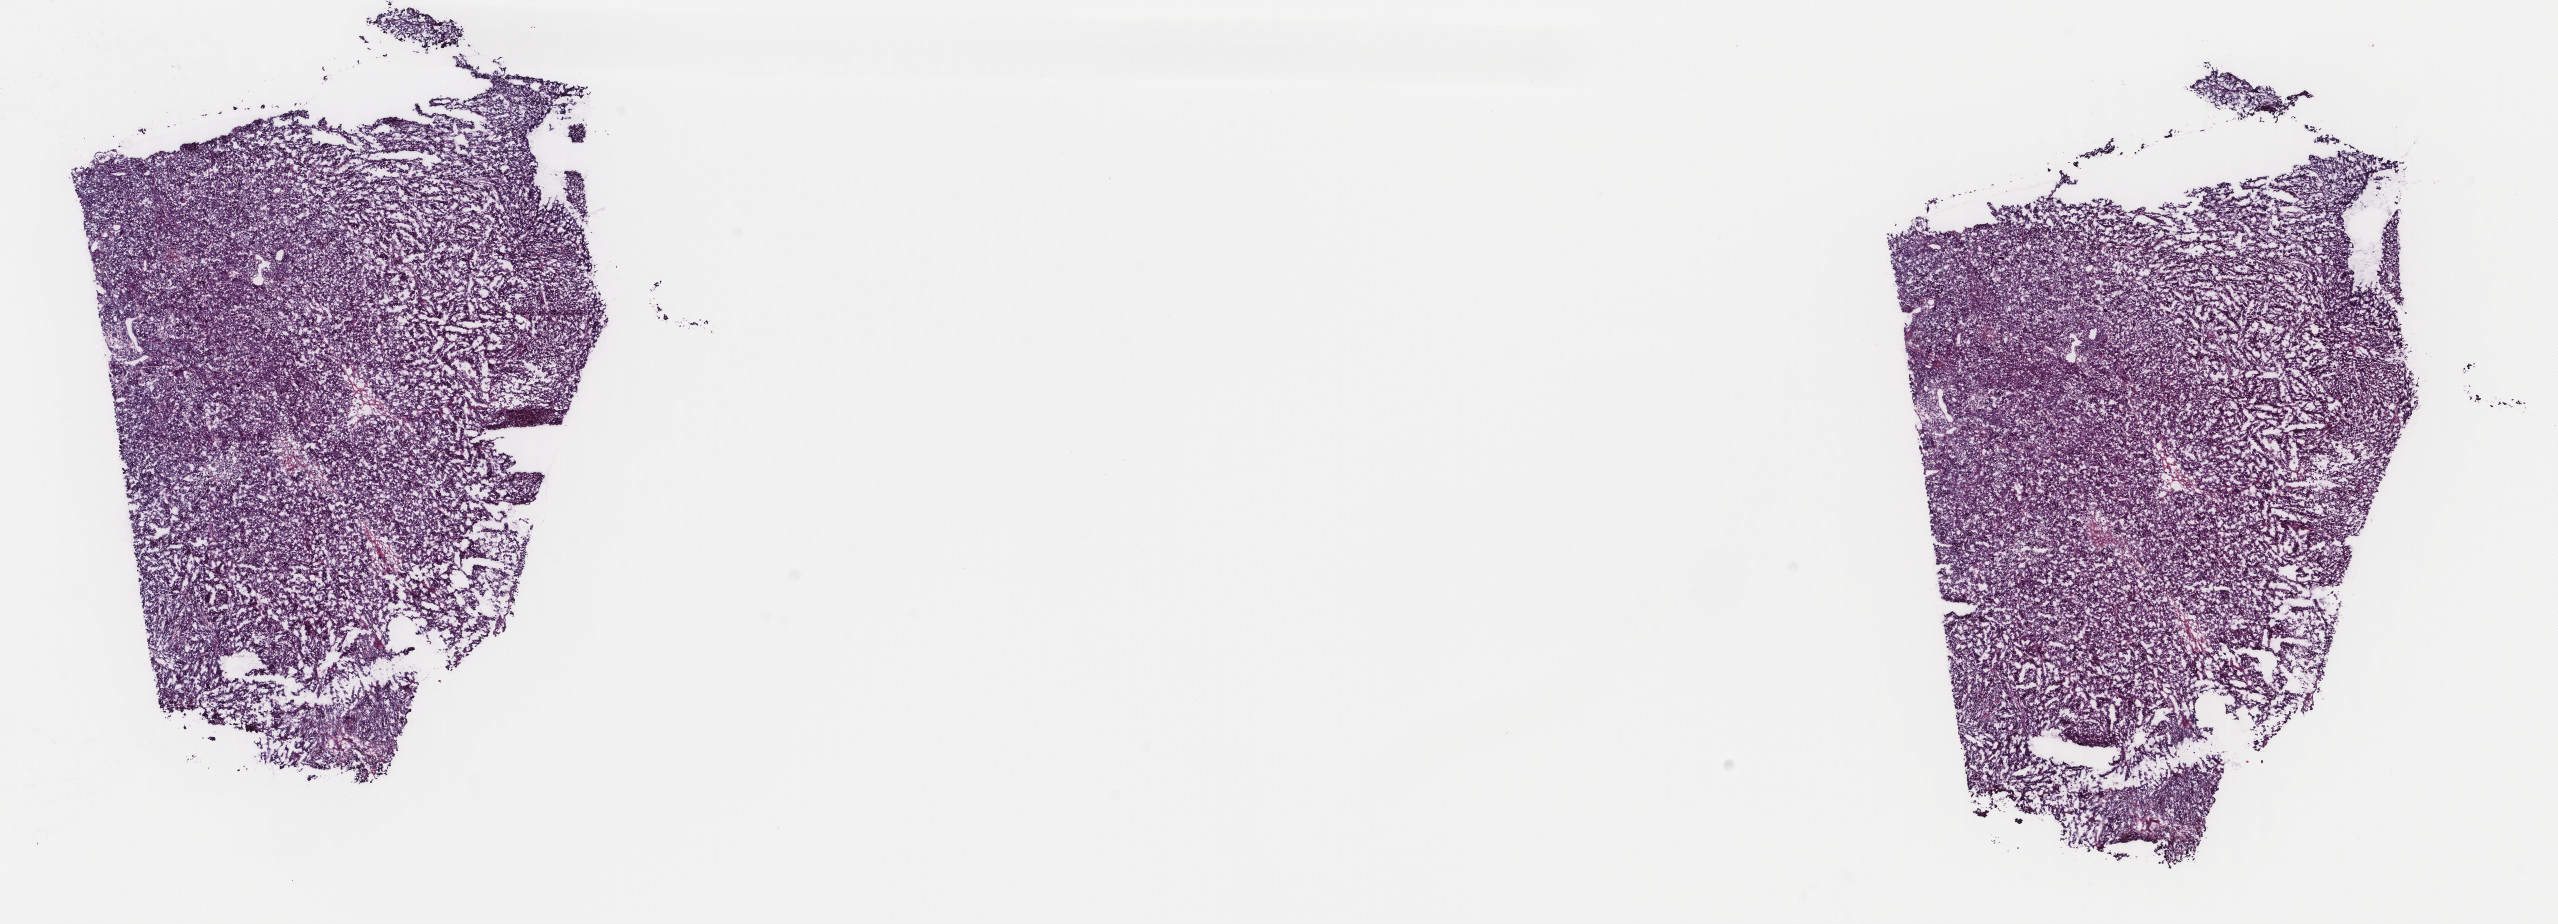
Whole-slide histology image, H&E, shown as a low-resolution overview of the whole scanned area (about 20.3 x 7.3 mm, from a 40x scan), frozen section, metastatic tumour sample, sampled site: lymph nodes of axilla or arm. Patient: male, age at initial diagnosis 71 years. Slide review estimates, as recorded: tumour cells 100%, tumour nuclei 95%, normal cells 0%, stromal cells 0%, necrosis 0%. Inflammatory infiltration, as recorded: lymphocyte infiltration 0%, monocyte infiltration 0%, neutrophil infiltration 0%.
• this section: metastatic tumour tissue
• patient diagnosis: Malignant melanoma, NOS